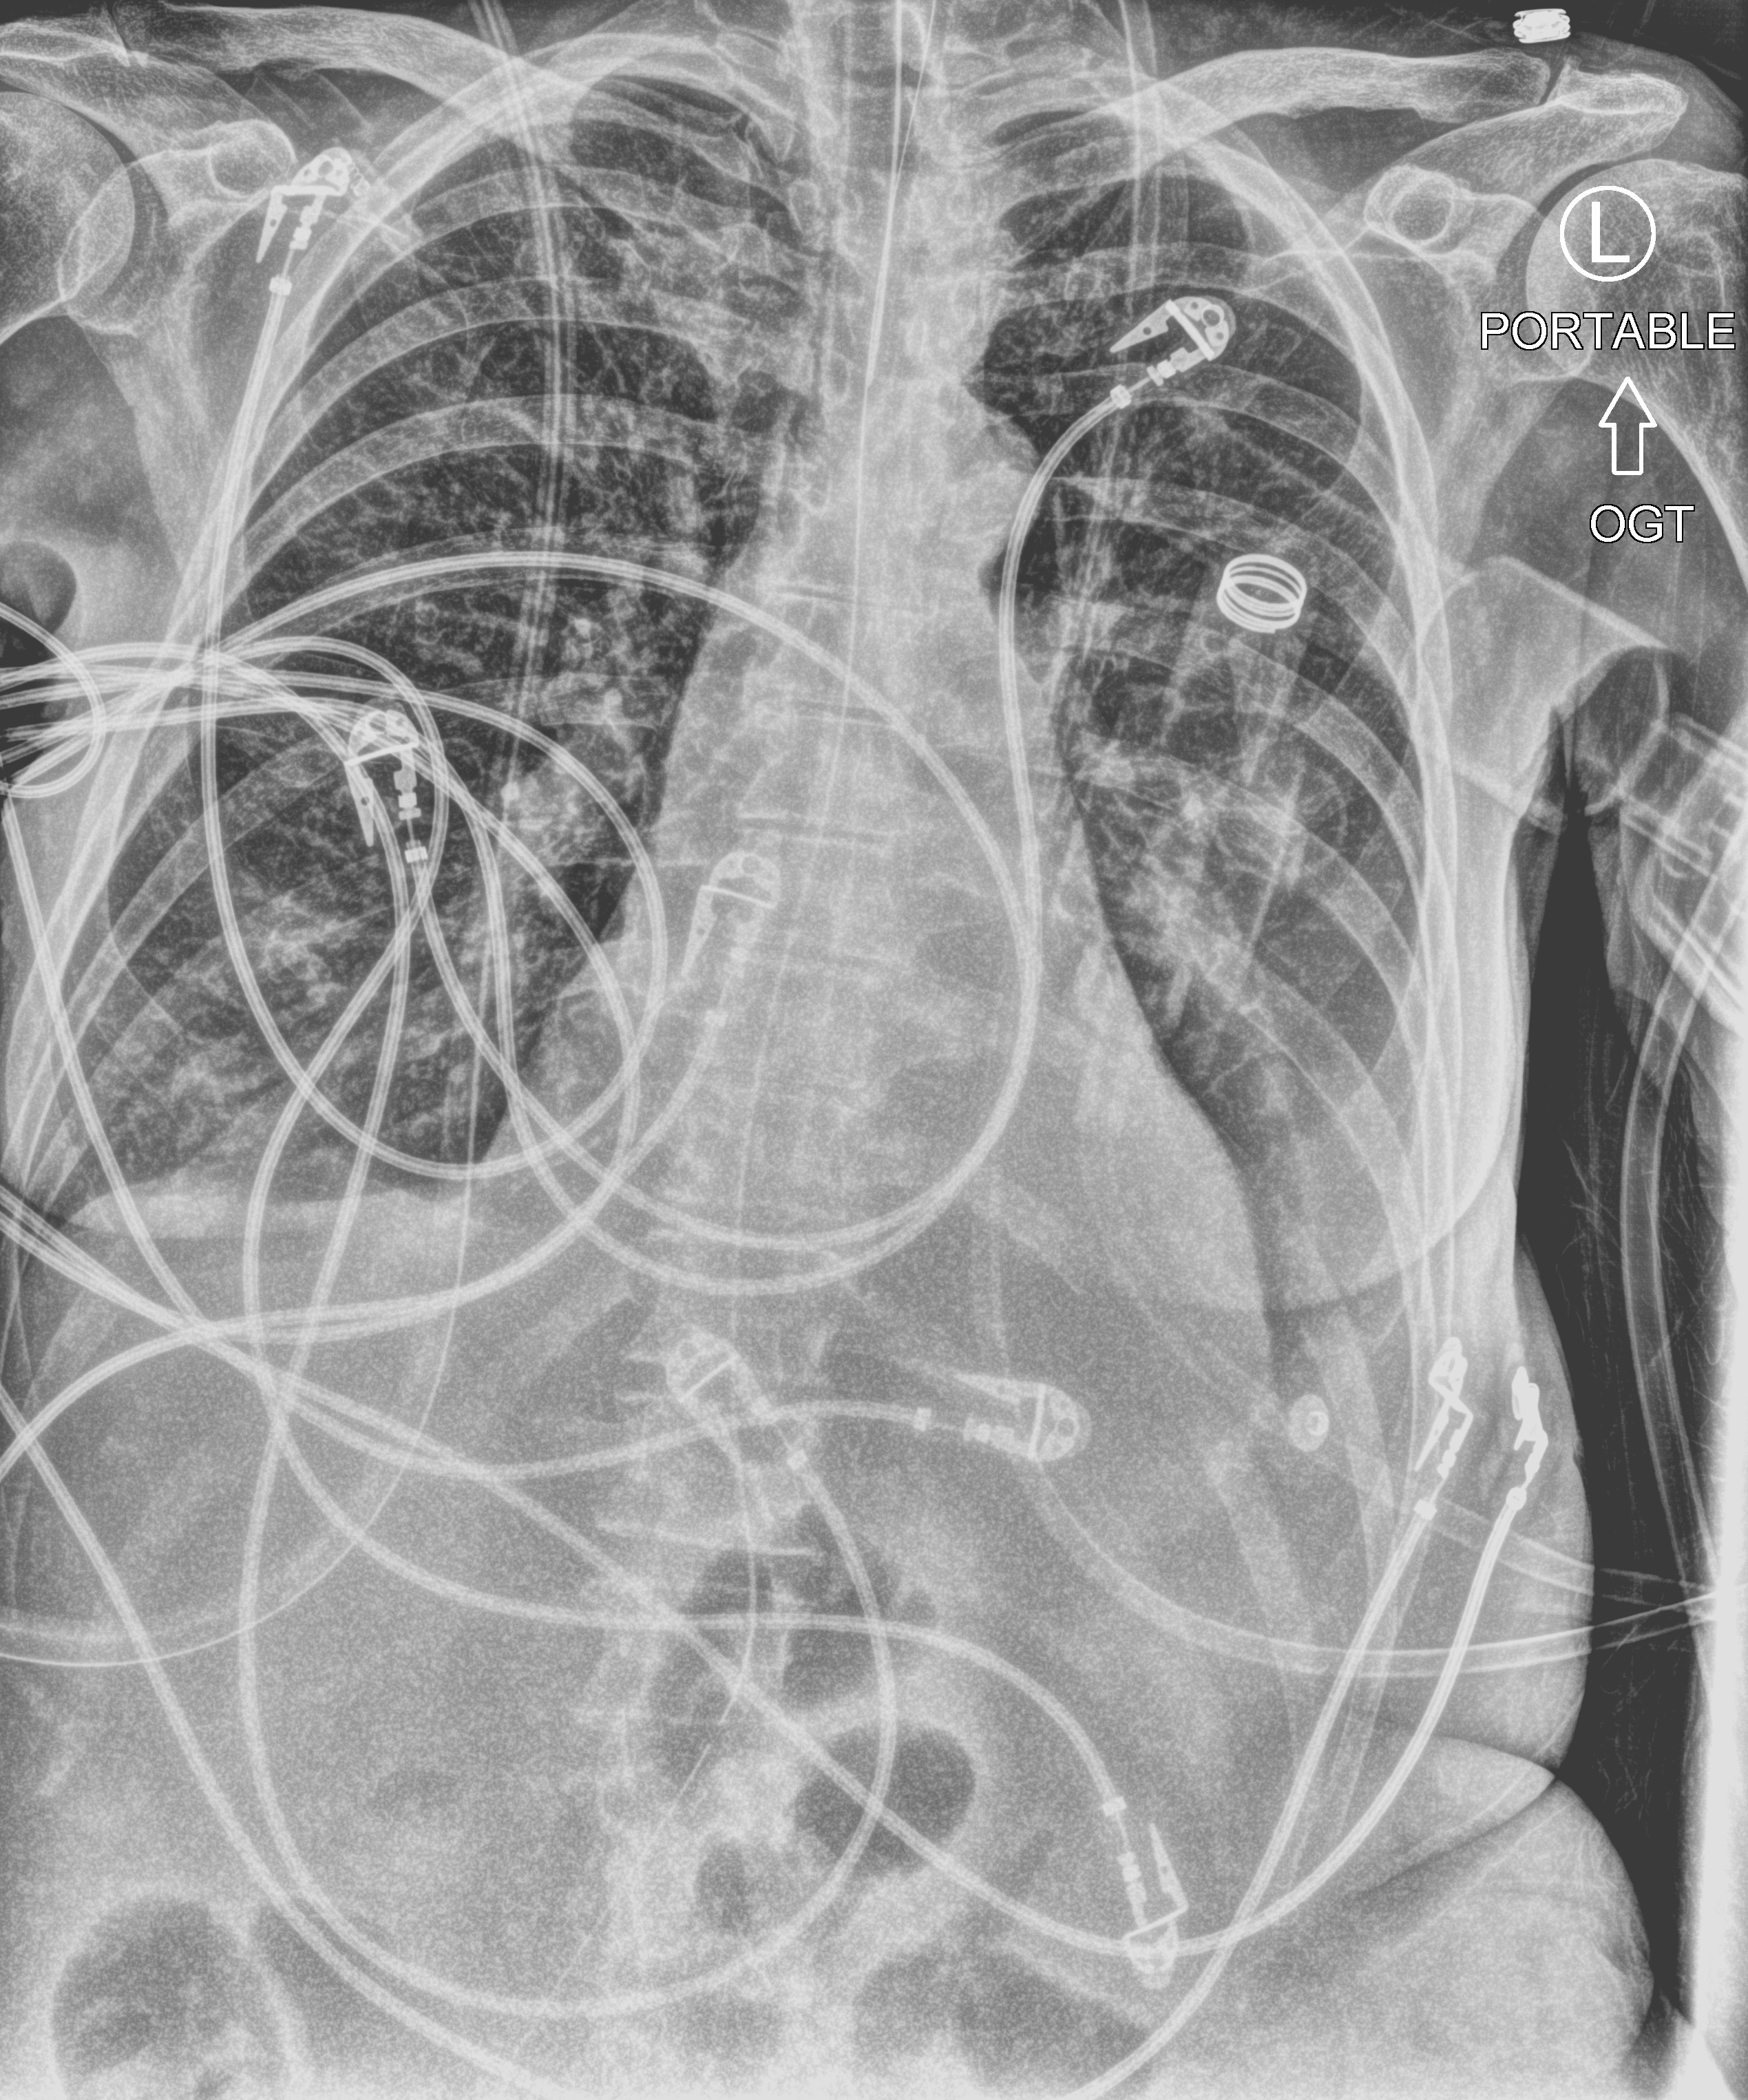
Chest X-ray (portable), anteroposterior (AP) projection. Patient hospitalised with COVID-19; female, aged 60–74 years.
Hospital-stay facts (about this admission, not read from this image; timing relative to this image not recorded): mechanically ventilated during this hospital stay: yes.